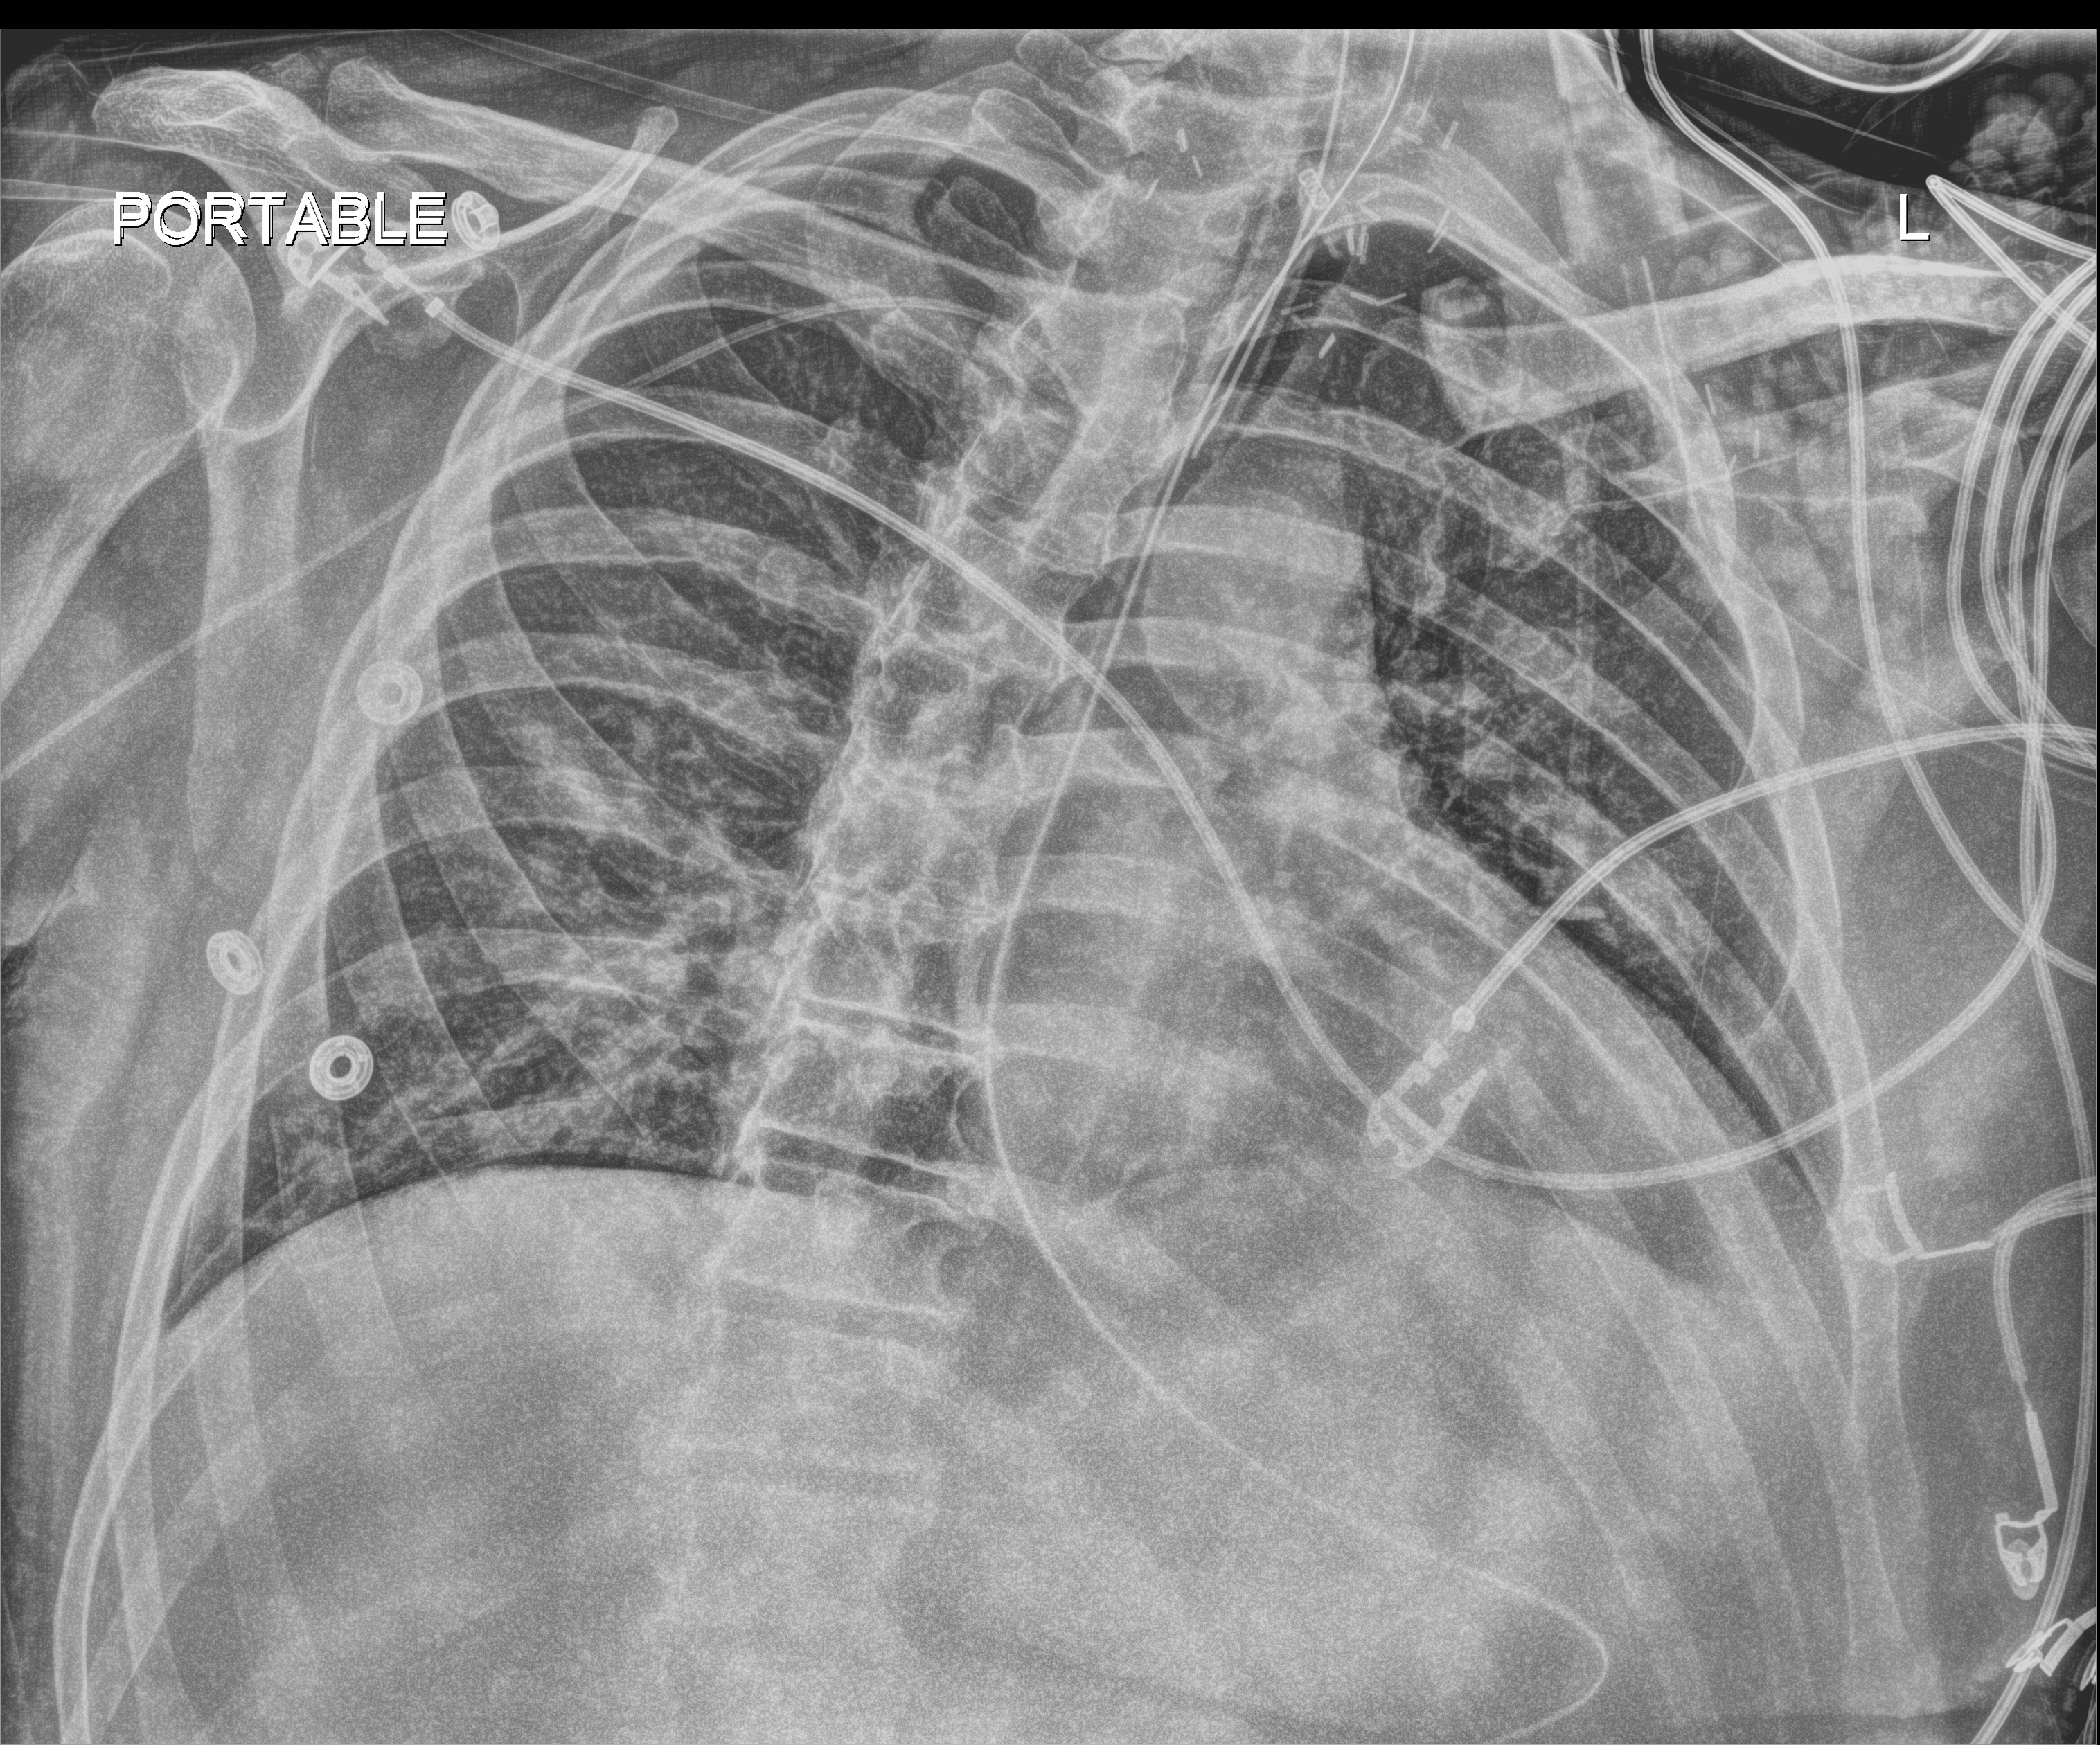
Portable chest radiograph; anteroposterior (AP) projection. Patient hospitalised with COVID-19, aged 18–59 years.
From the hospital-stay record, not from the radiograph (when in the stay this image was taken is not recorded):
- chronic kidney disease (admission record): yes
- mechanically ventilated during this hospital stay: yes
- smoking status (admission record): never